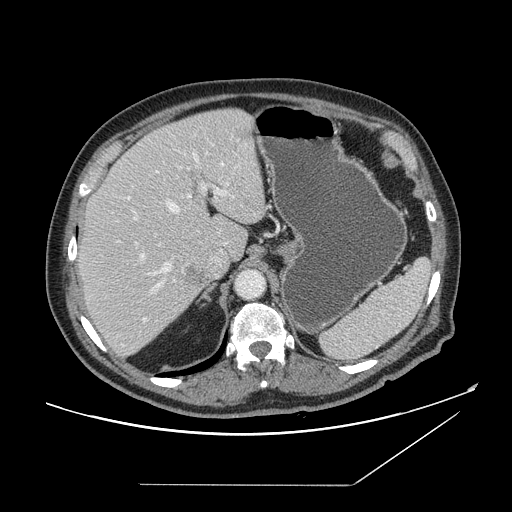
Contrast-enhanced abdominal CT, one axial slice; slice 111 of 166 in the series (ordered by position); intravenous contrast given; soft-tissue window (W 400 / L 40 HU); 512 × 512 image matrix. Male patient, age 80 years. Case-level facts recorded for this patient, not image findings: diagnosis: colorectal cancer liver metastases, imaged before liver resection; multiple liver metastases: no; largest metastasis: 2.2 cm; disease in both lobes: no.
Outlined on this slice (outlined manually by an expert reader):
- hepatic veins: box from (x=135, y=153) to (x=223, y=294) px
- liver: (x=78, y=109)–(x=266, y=356)
- planned liver remnant (the part of the liver to remain after resection): (x=85, y=109)–(x=266, y=260)
- portal vein (with intrahepatic branches): (x=129, y=145)–(x=226, y=321)
- liver metastasis: (x=187, y=269)–(x=205, y=287)
- liver metastasis: (x=184, y=266)–(x=205, y=285)